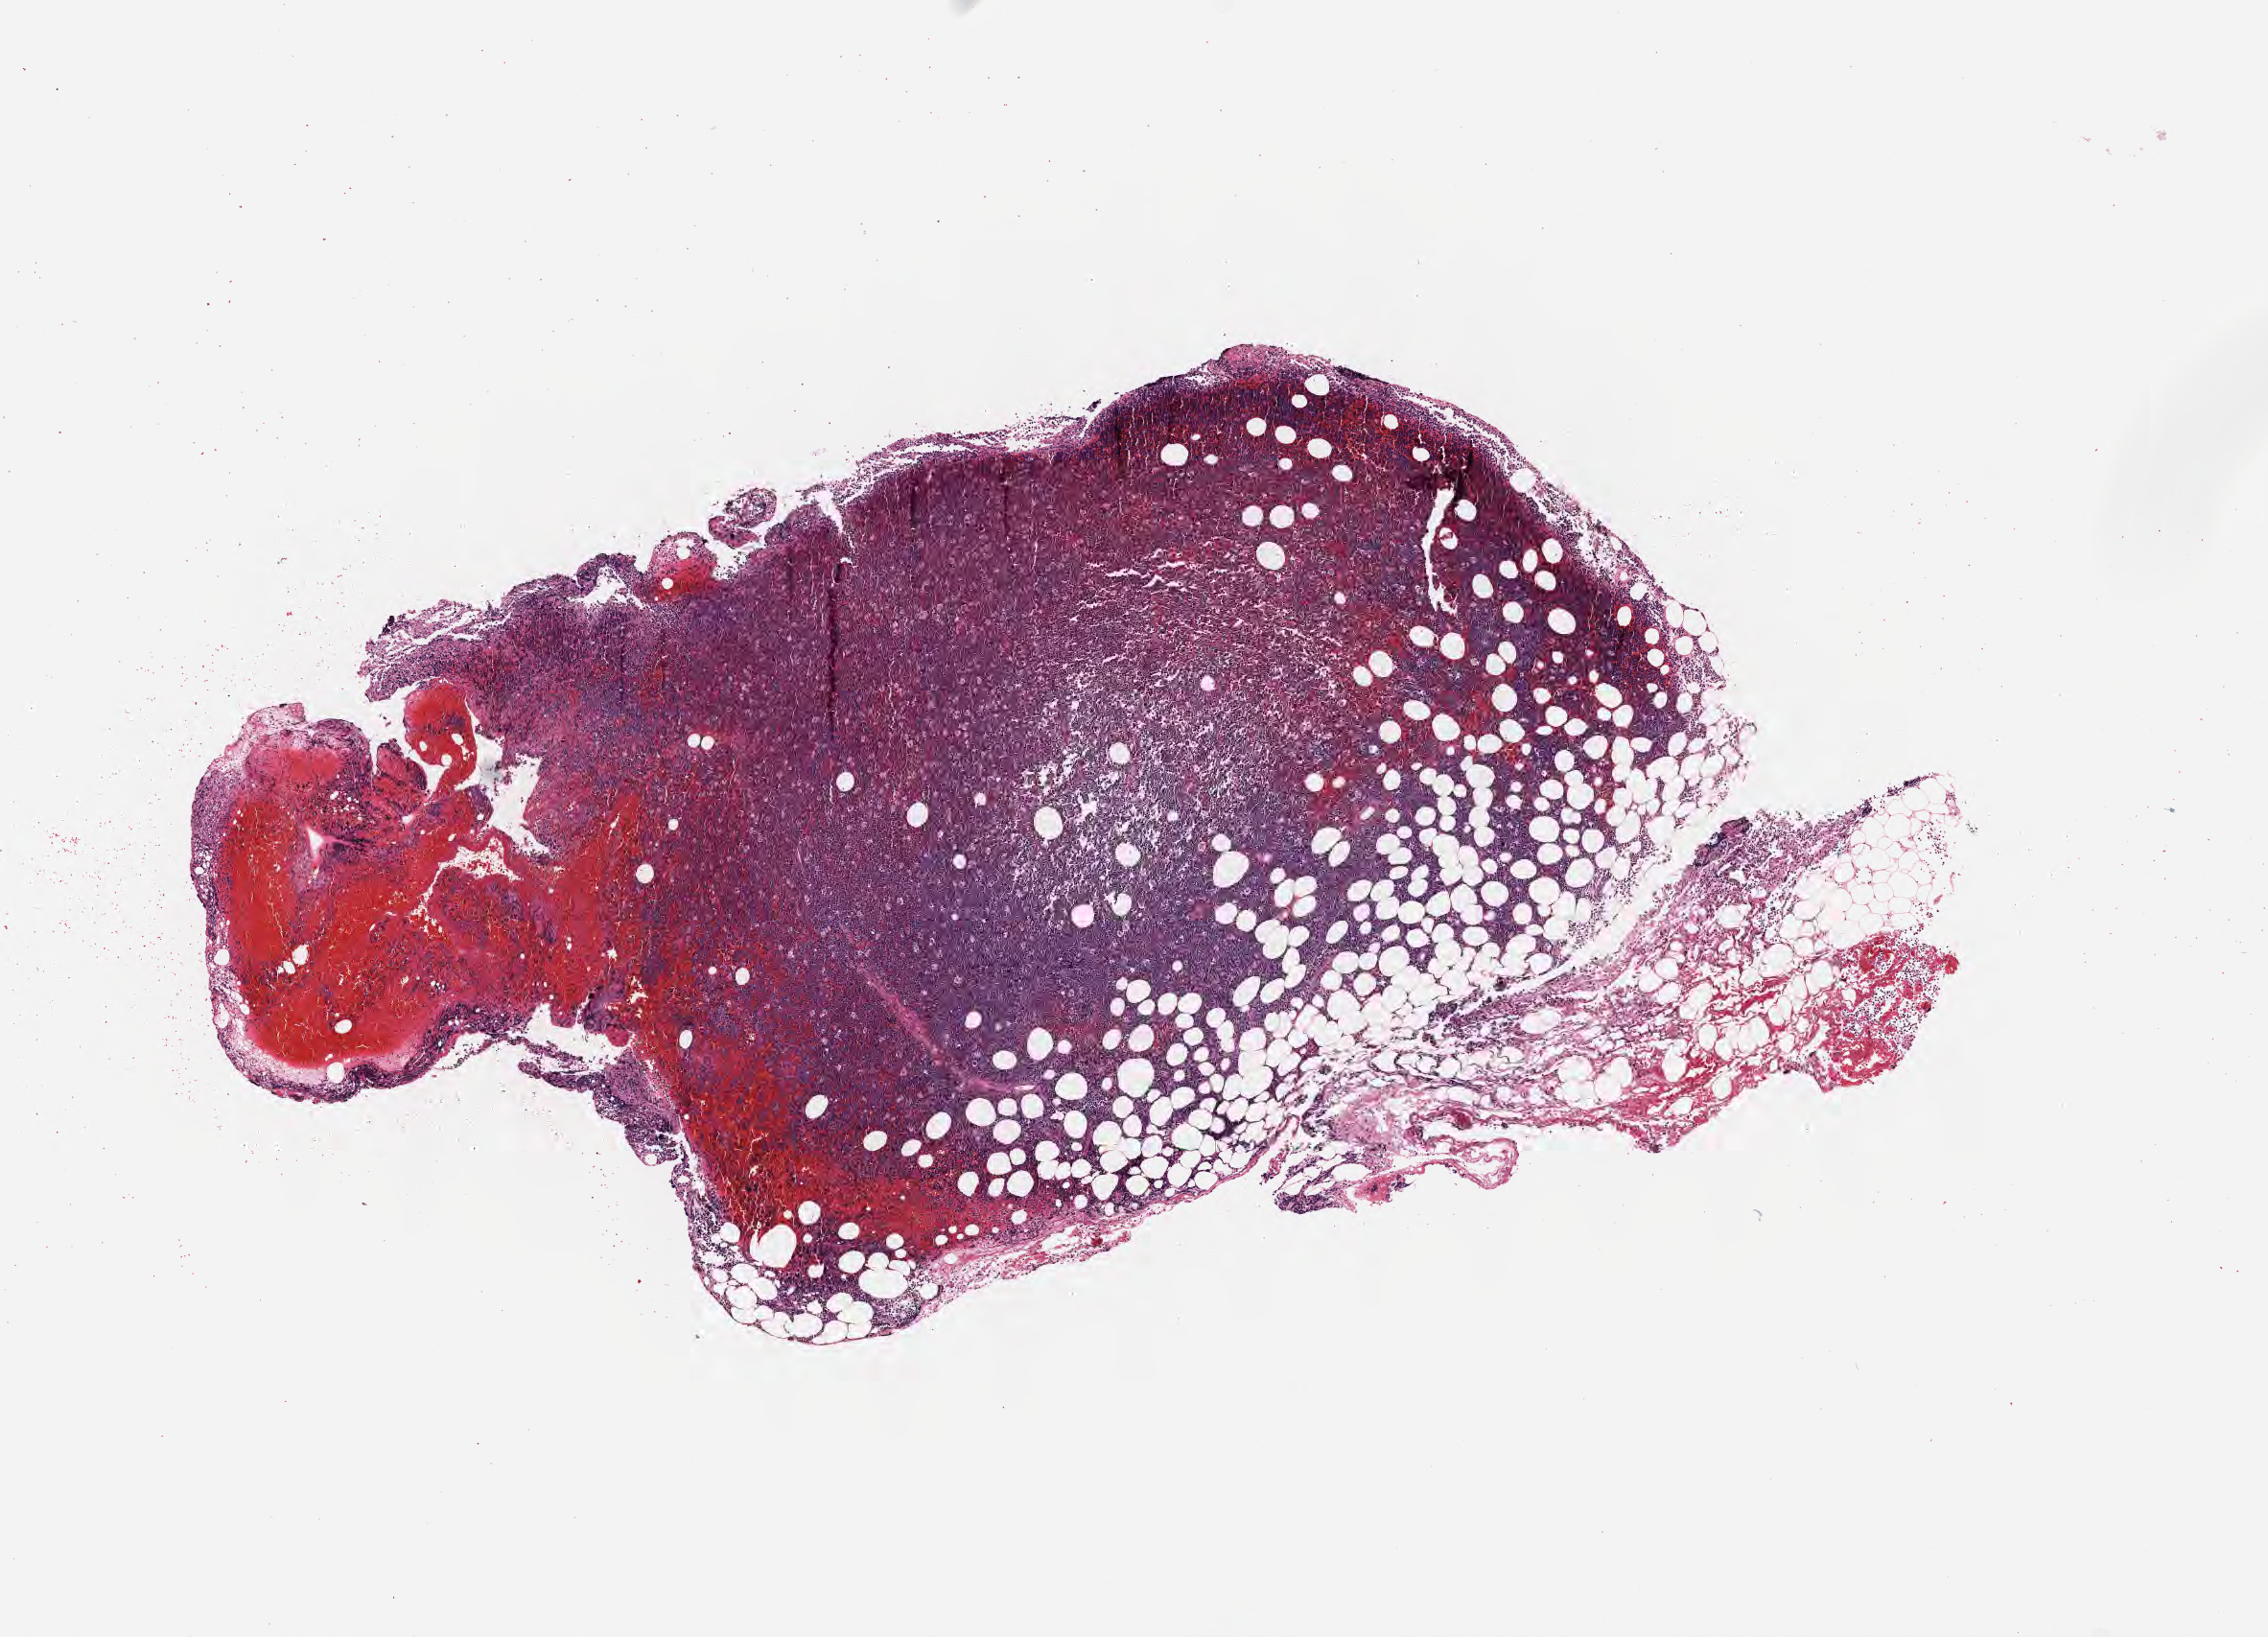
Whole-slide image, haematoxylin and eosin stain, whole scanned area (about 9.6 x 6.9 mm) shown as a low-resolution overview; FFPE section; specimen: primary tumor; anatomic site: bone marrow. Male patient, age 70 years. Slide review estimates, as recorded: tumor cells 85%, tumor nuclei 90%, stromal cells 10%, necrosis 5%, normal cells 0%. Infiltration values recorded for this section: lymphocyte infiltration 10%, monocyte infiltration 40%, neutrophil infiltration 10%.
Diagnosis: Neoplasm, uncertain whether benign or malignant. Ann Arbor stage (patient): Stage IV.